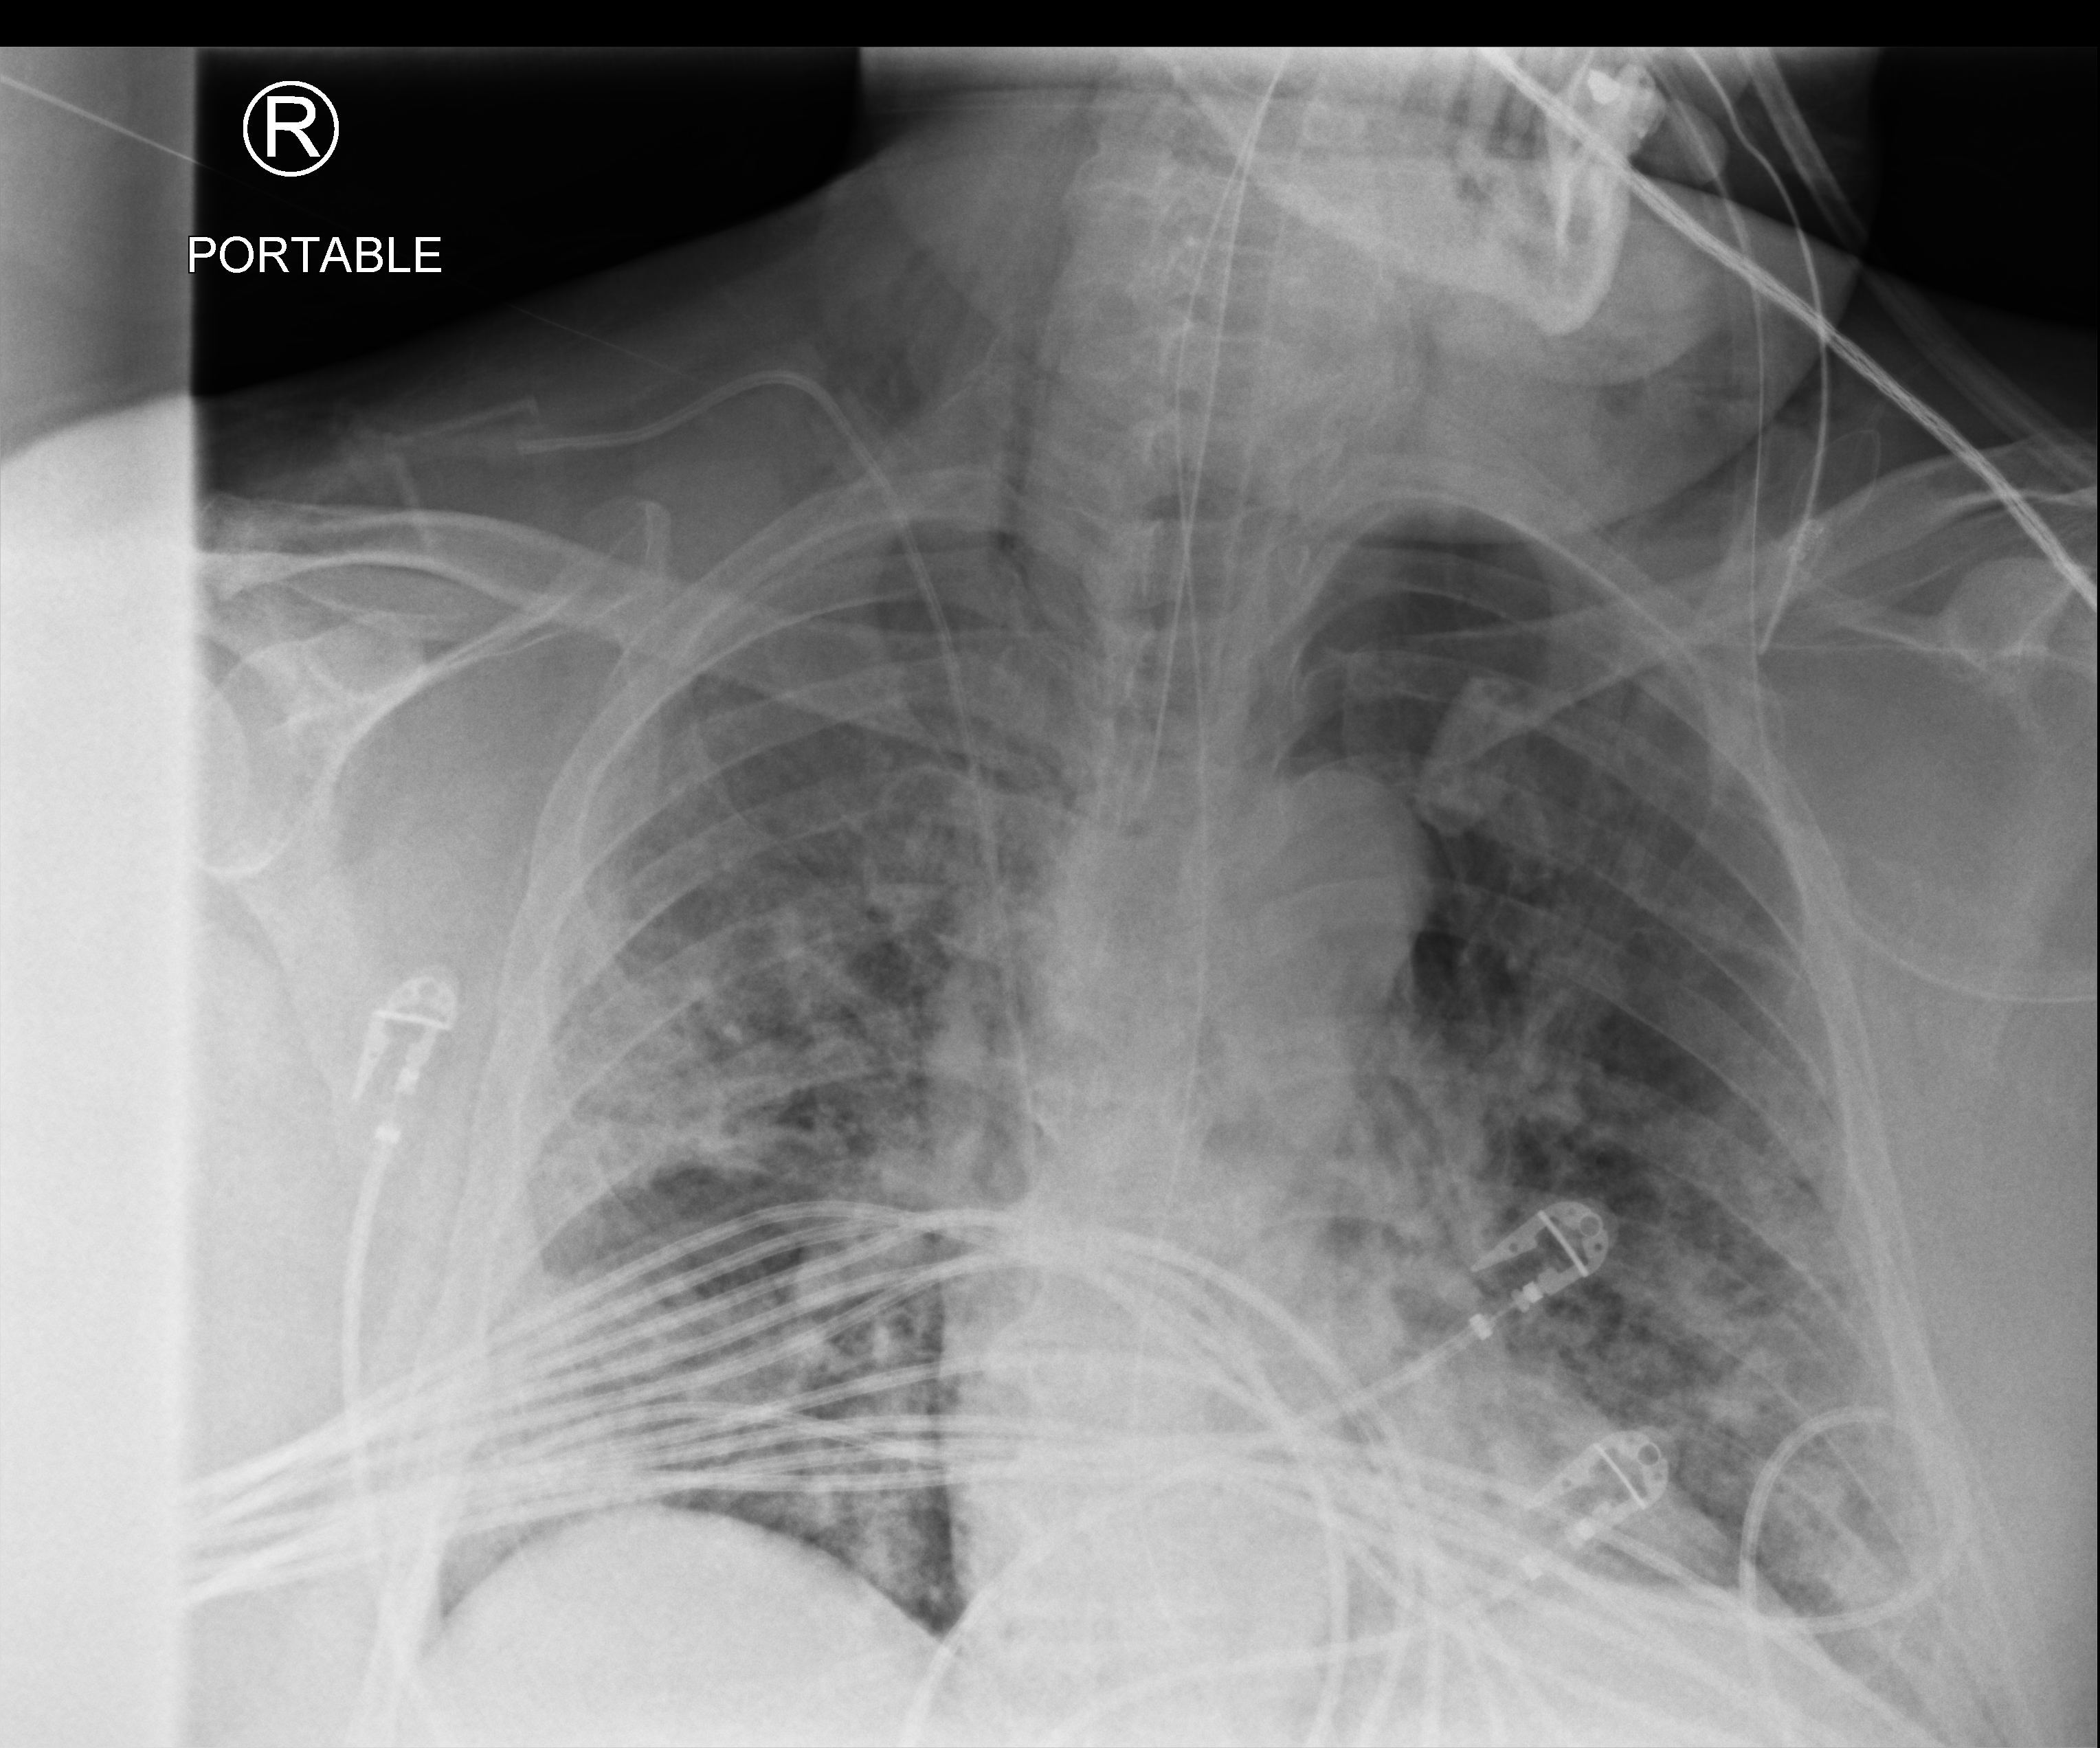
Chest X-ray (portable); anteroposterior (AP) projection. Patient hospitalised with COVID-19, aged 18–59 years.
Admission-level facts for this patient (not findings on this image; timing relative to this image not recorded):
- smoking status (admission record): never
- mechanically ventilated during this hospital stay: yes
- admitted to intensive care during this hospital stay: yes